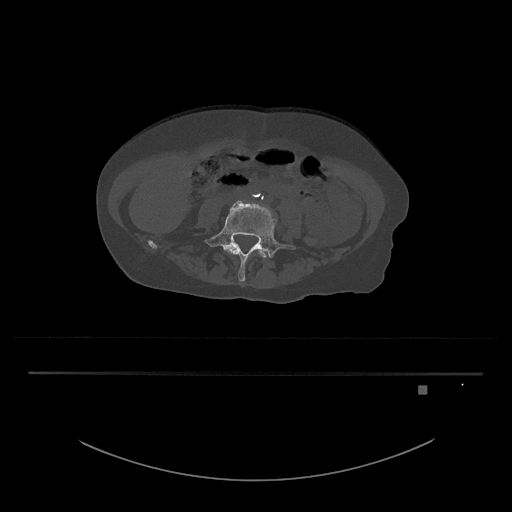
CT including the spine, one axial slice. Slice 316 of 797 in the series (ordered by position). Reconstruction kernel Br40s/3. Bone window (W 1800 / L 400 HU). 0.5 mm slice thickness. 512 × 512 image matrix, field of view 500 × 500 mm. Patient: female, 57 years. From the clinical record (not read from this slice): primary cancer: cervical.
Structures marked on this image (semi-automatic segmentation, software-assisted and operator-edited):
- L4 vertebra: bounding box <224,242,269,258> (left, top, right, bottom; pixels)